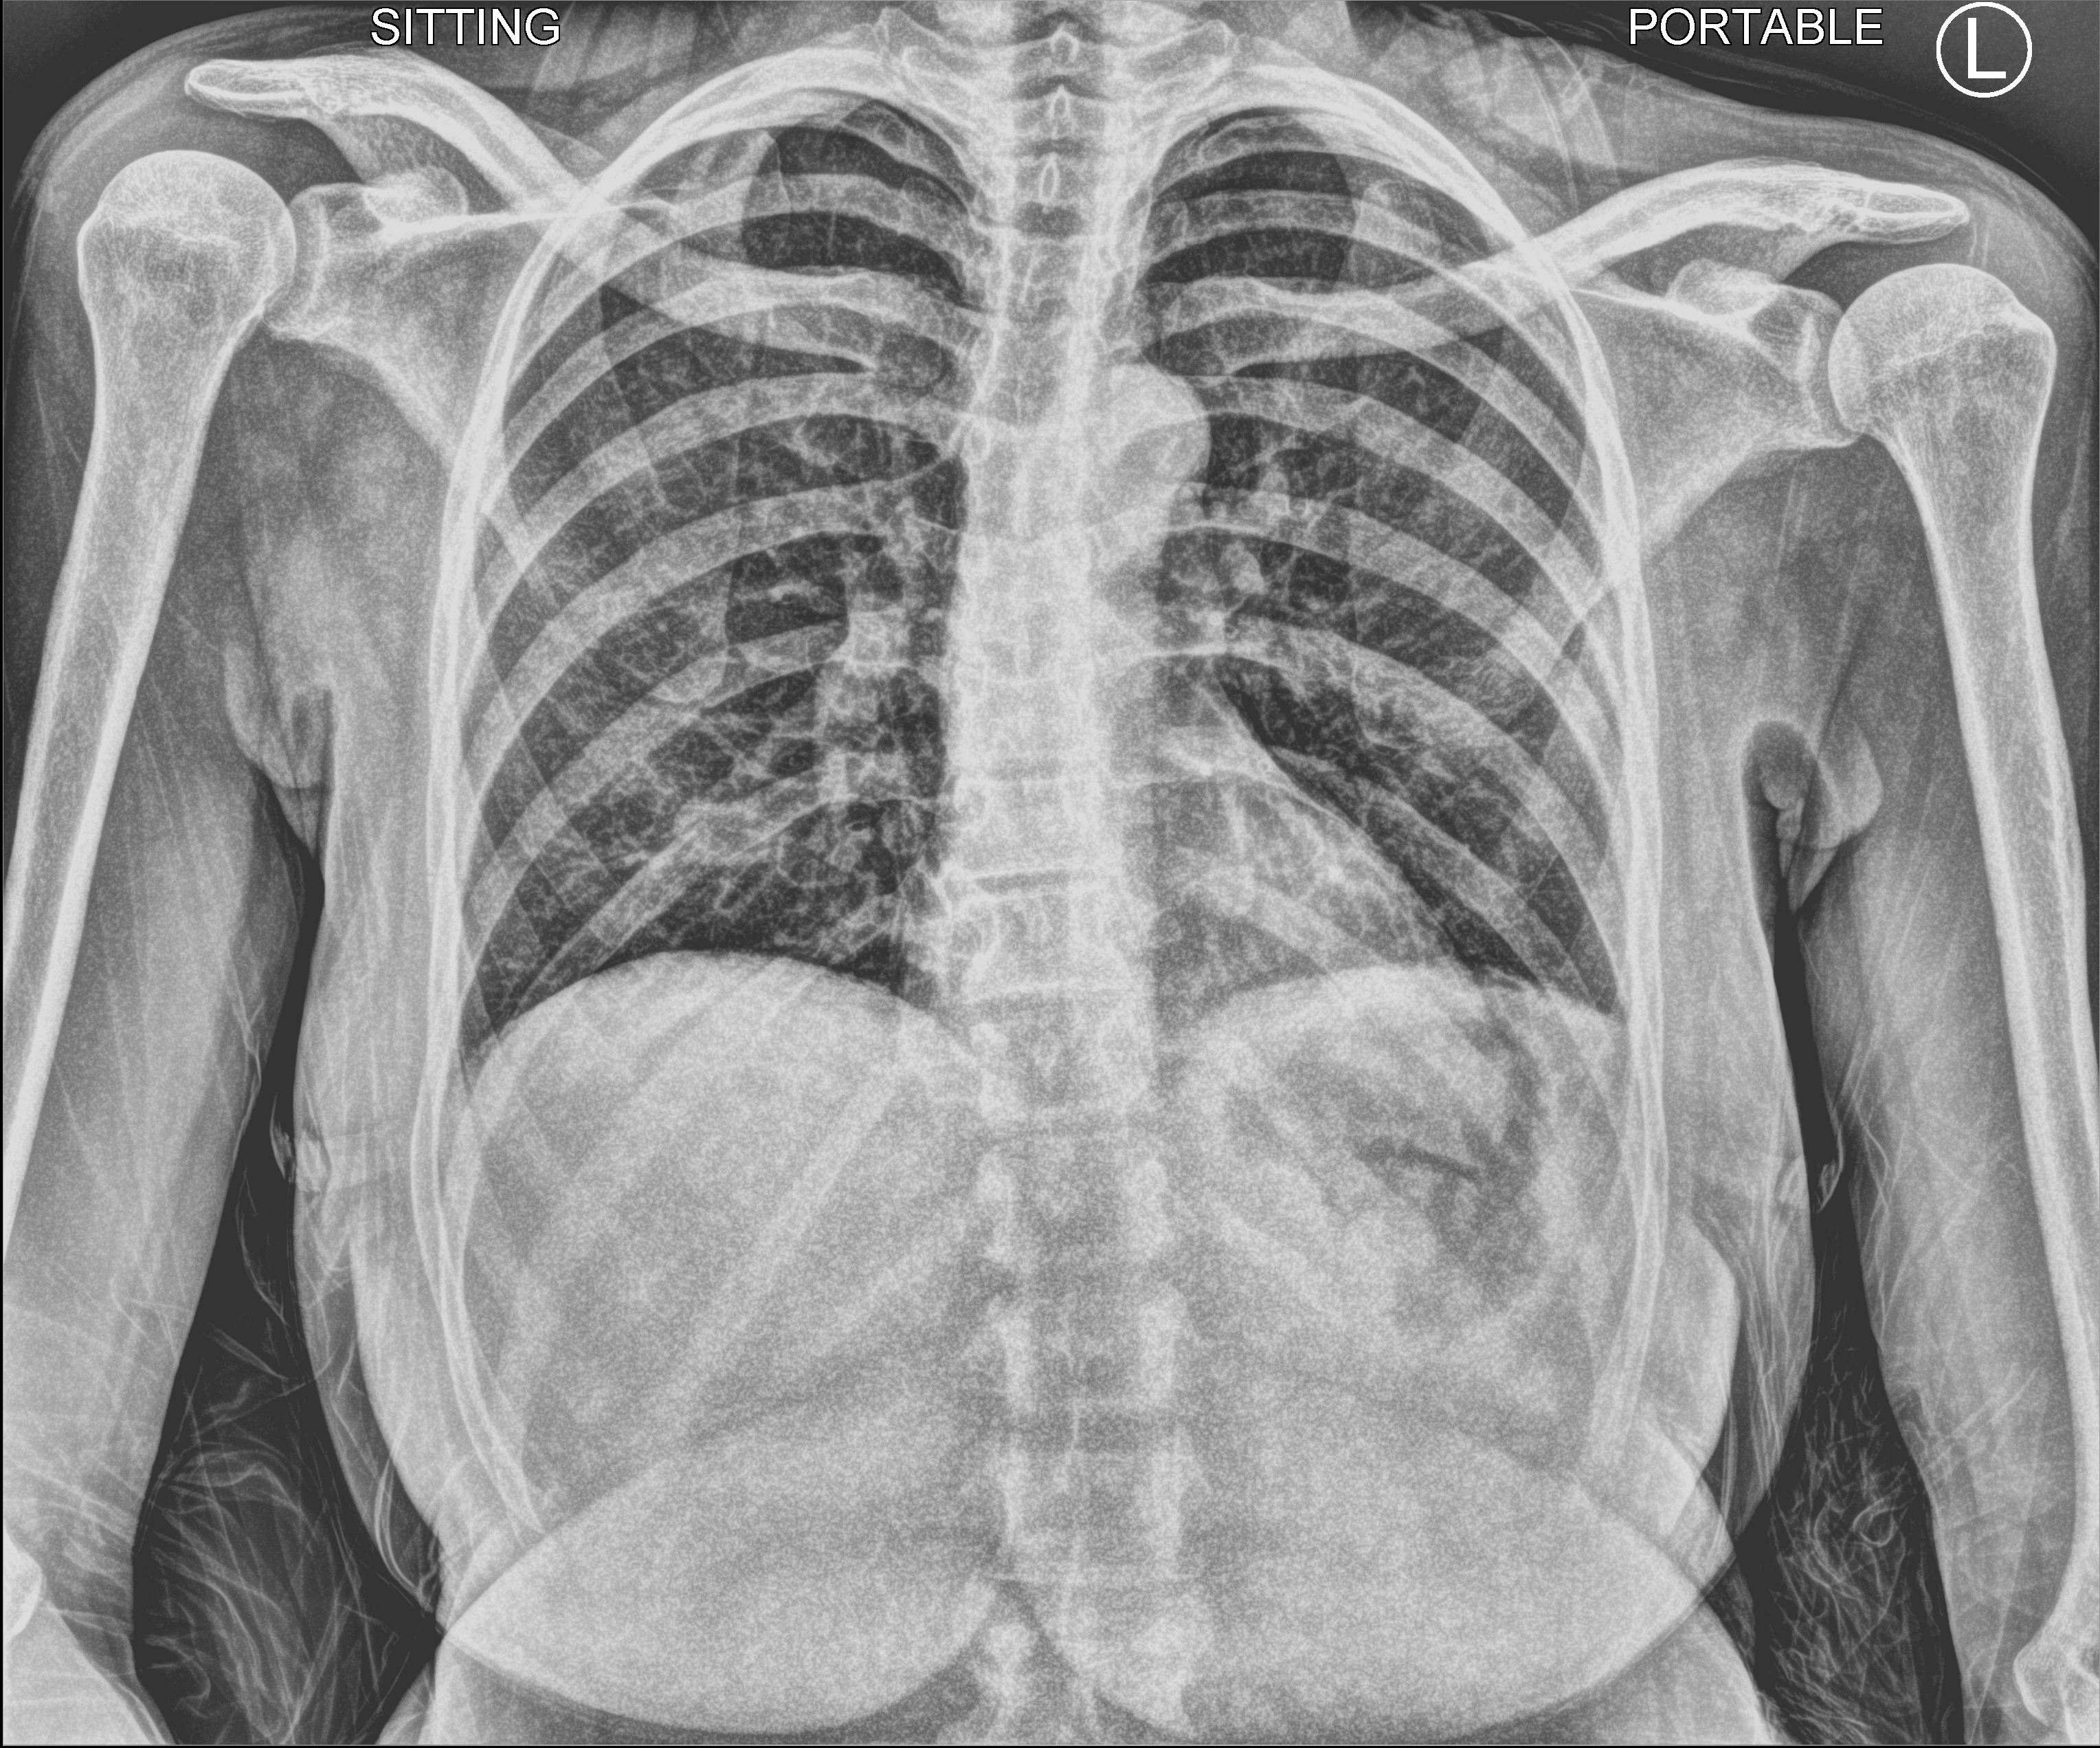
Bedside chest radiograph (computed radiography); anteroposterior (AP) projection. Female patient hospitalised with COVID-19, age 18–59 years.
From the hospital-stay record, not from the radiograph (when in the stay this image was taken is not recorded): admitted to intensive care during this hospital stay: no.